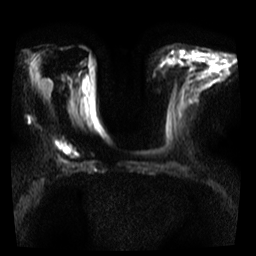
Breast MRI, one axial slice; position 14 of 35 along the scan axis; diffusion-weighted series; image 2 of 4 stored at this slice position (different b-values; order by instance number); 3 T; 5 mm slice thickness; 256 × 256 image matrix, field of view 300 × 300 mm. Female patient.
Outlined on this slice (outlined manually by an expert reader):
- tumour on diffusion-weighted imaging: bounding box [x1, y1, x2, y2] px = [53, 134, 80, 158]